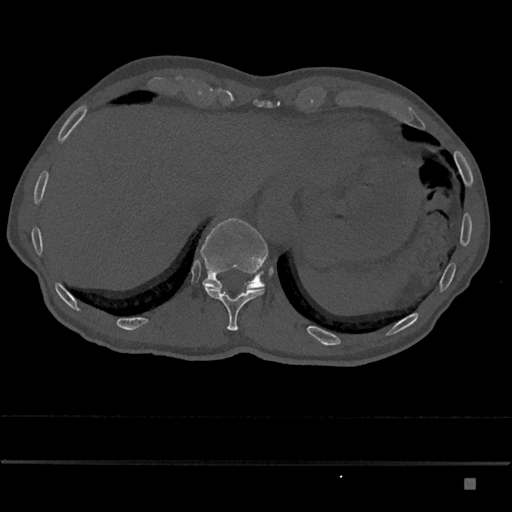
CT including the spine, one axial slice. Slice 651 of 797 in the series (ordered by position). Bone window (W 1800 / L 400 HU). 0.5 mm slice thickness. 512 × 512 image matrix, field of view 390 × 390 mm. Patient: male, 72 years. From the clinical record (not read from this slice): primary cancer: prostate.
Annotated regions visible in this slice (semi-automatic segmentation, software-assisted and operator-edited):
- T11 vertebra: bounding box <202,283,265,331> (left, top, right, bottom; pixels)
- T12 vertebra: <200,218,268,289>